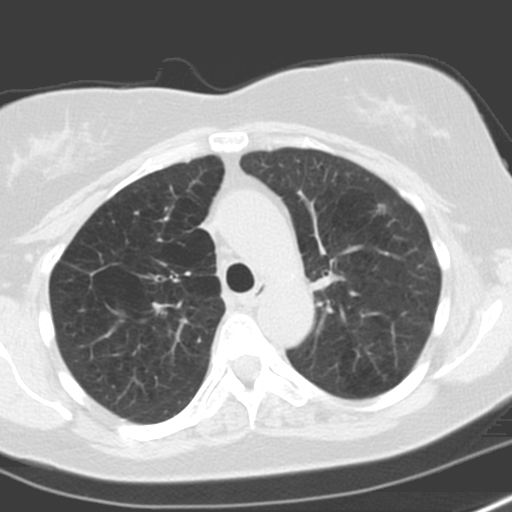
Low-dose screening chest CT, axial slice. First (baseline) screen. Lung window (W 1500 / L -600 HU). 3.2 mm slice thickness. Standard (soft-tissue) reconstruction kernel (C). 120 kVp. Slice 54 of 173 in the series. 512 × 512 image matrix. Female participant, aged 57 years at enrolment. Former smoker at enrolment.
Lesion marked by an expert reader, bounding box <359,197,400,229> (left, top, right, bottom; pixels). Screening reader's record for this exam: no non-calcified nodule ≥4 mm recorded.